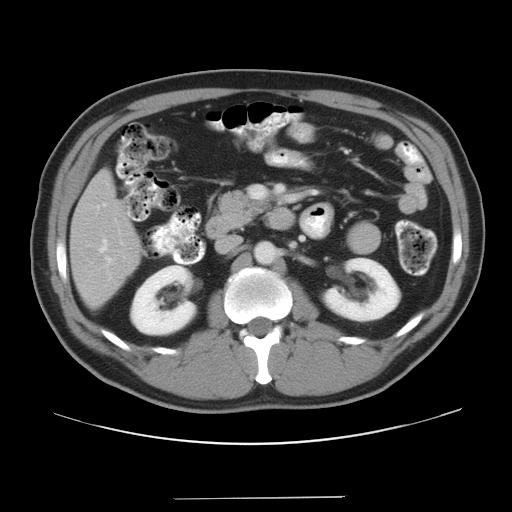
Contrast-enhanced abdominal CT, one axial slice. Position 16 of 37 along the scan axis. Reconstruction kernel STANDARD. Intravenous contrast given. Soft-tissue window (W 400 / L 40 HU). 7.5 mm slice thickness. 512 × 512 image matrix. Male patient, age 46 years. Case-level facts recorded for this patient, not image findings: diagnosis: colorectal cancer liver metastases, imaged before liver resection; multiple liver metastases: yes; largest metastasis: 1 cm.
Annotated regions visible in this slice (manually delineated by an expert):
- hepatic veins: bounding box <99,239,107,252> (left, top, right, bottom; pixels)
- liver: <72,173,139,307>
- planned liver remnant (the part of the liver to remain after resection): <72,173,139,307>